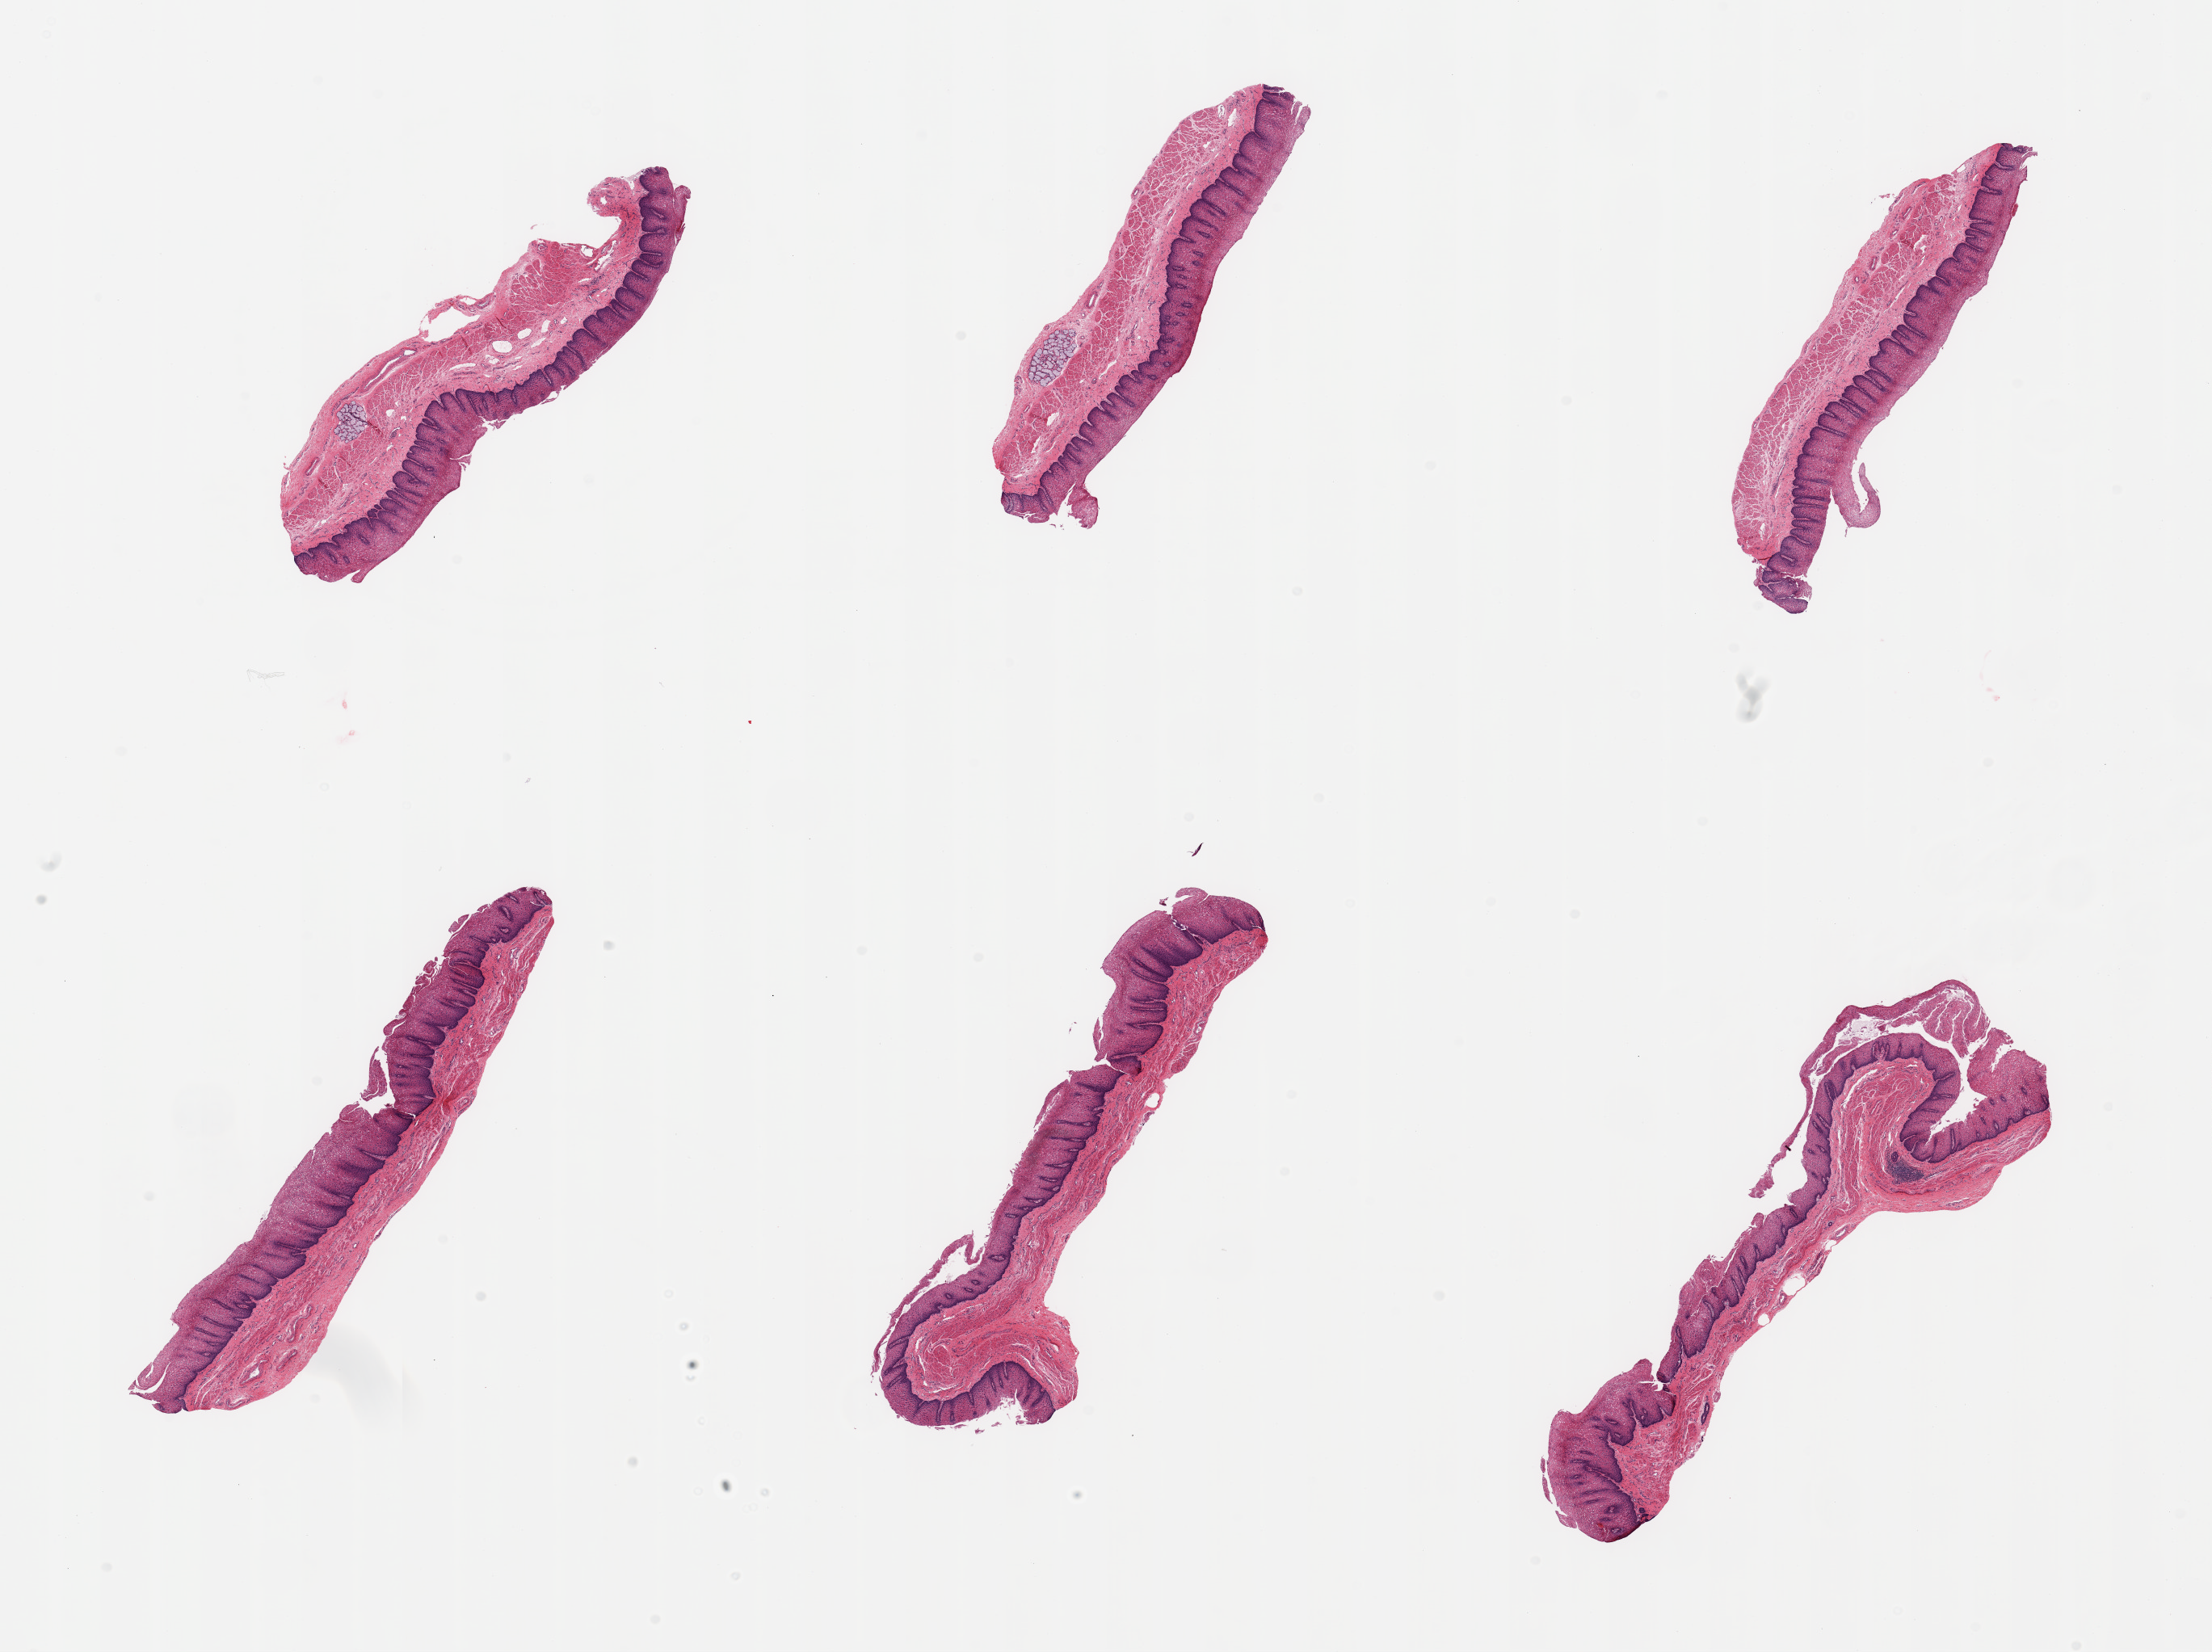
Whole-slide image, haematoxylin and eosin stain — low-resolution overview of the scanned area, about 21.7 x 16.2 mm (acquisition: 20x scan), PAXgene-fixed paraffin-embedded (PFPE) section, section of esophageal mucous membrane (target tissue), tissue donor sample. Donor: female.
Reviewer comment on this tissue sample: 6 pieces; basal epithelial hyperplasia (?reflux); superficial epithelial sloughing.